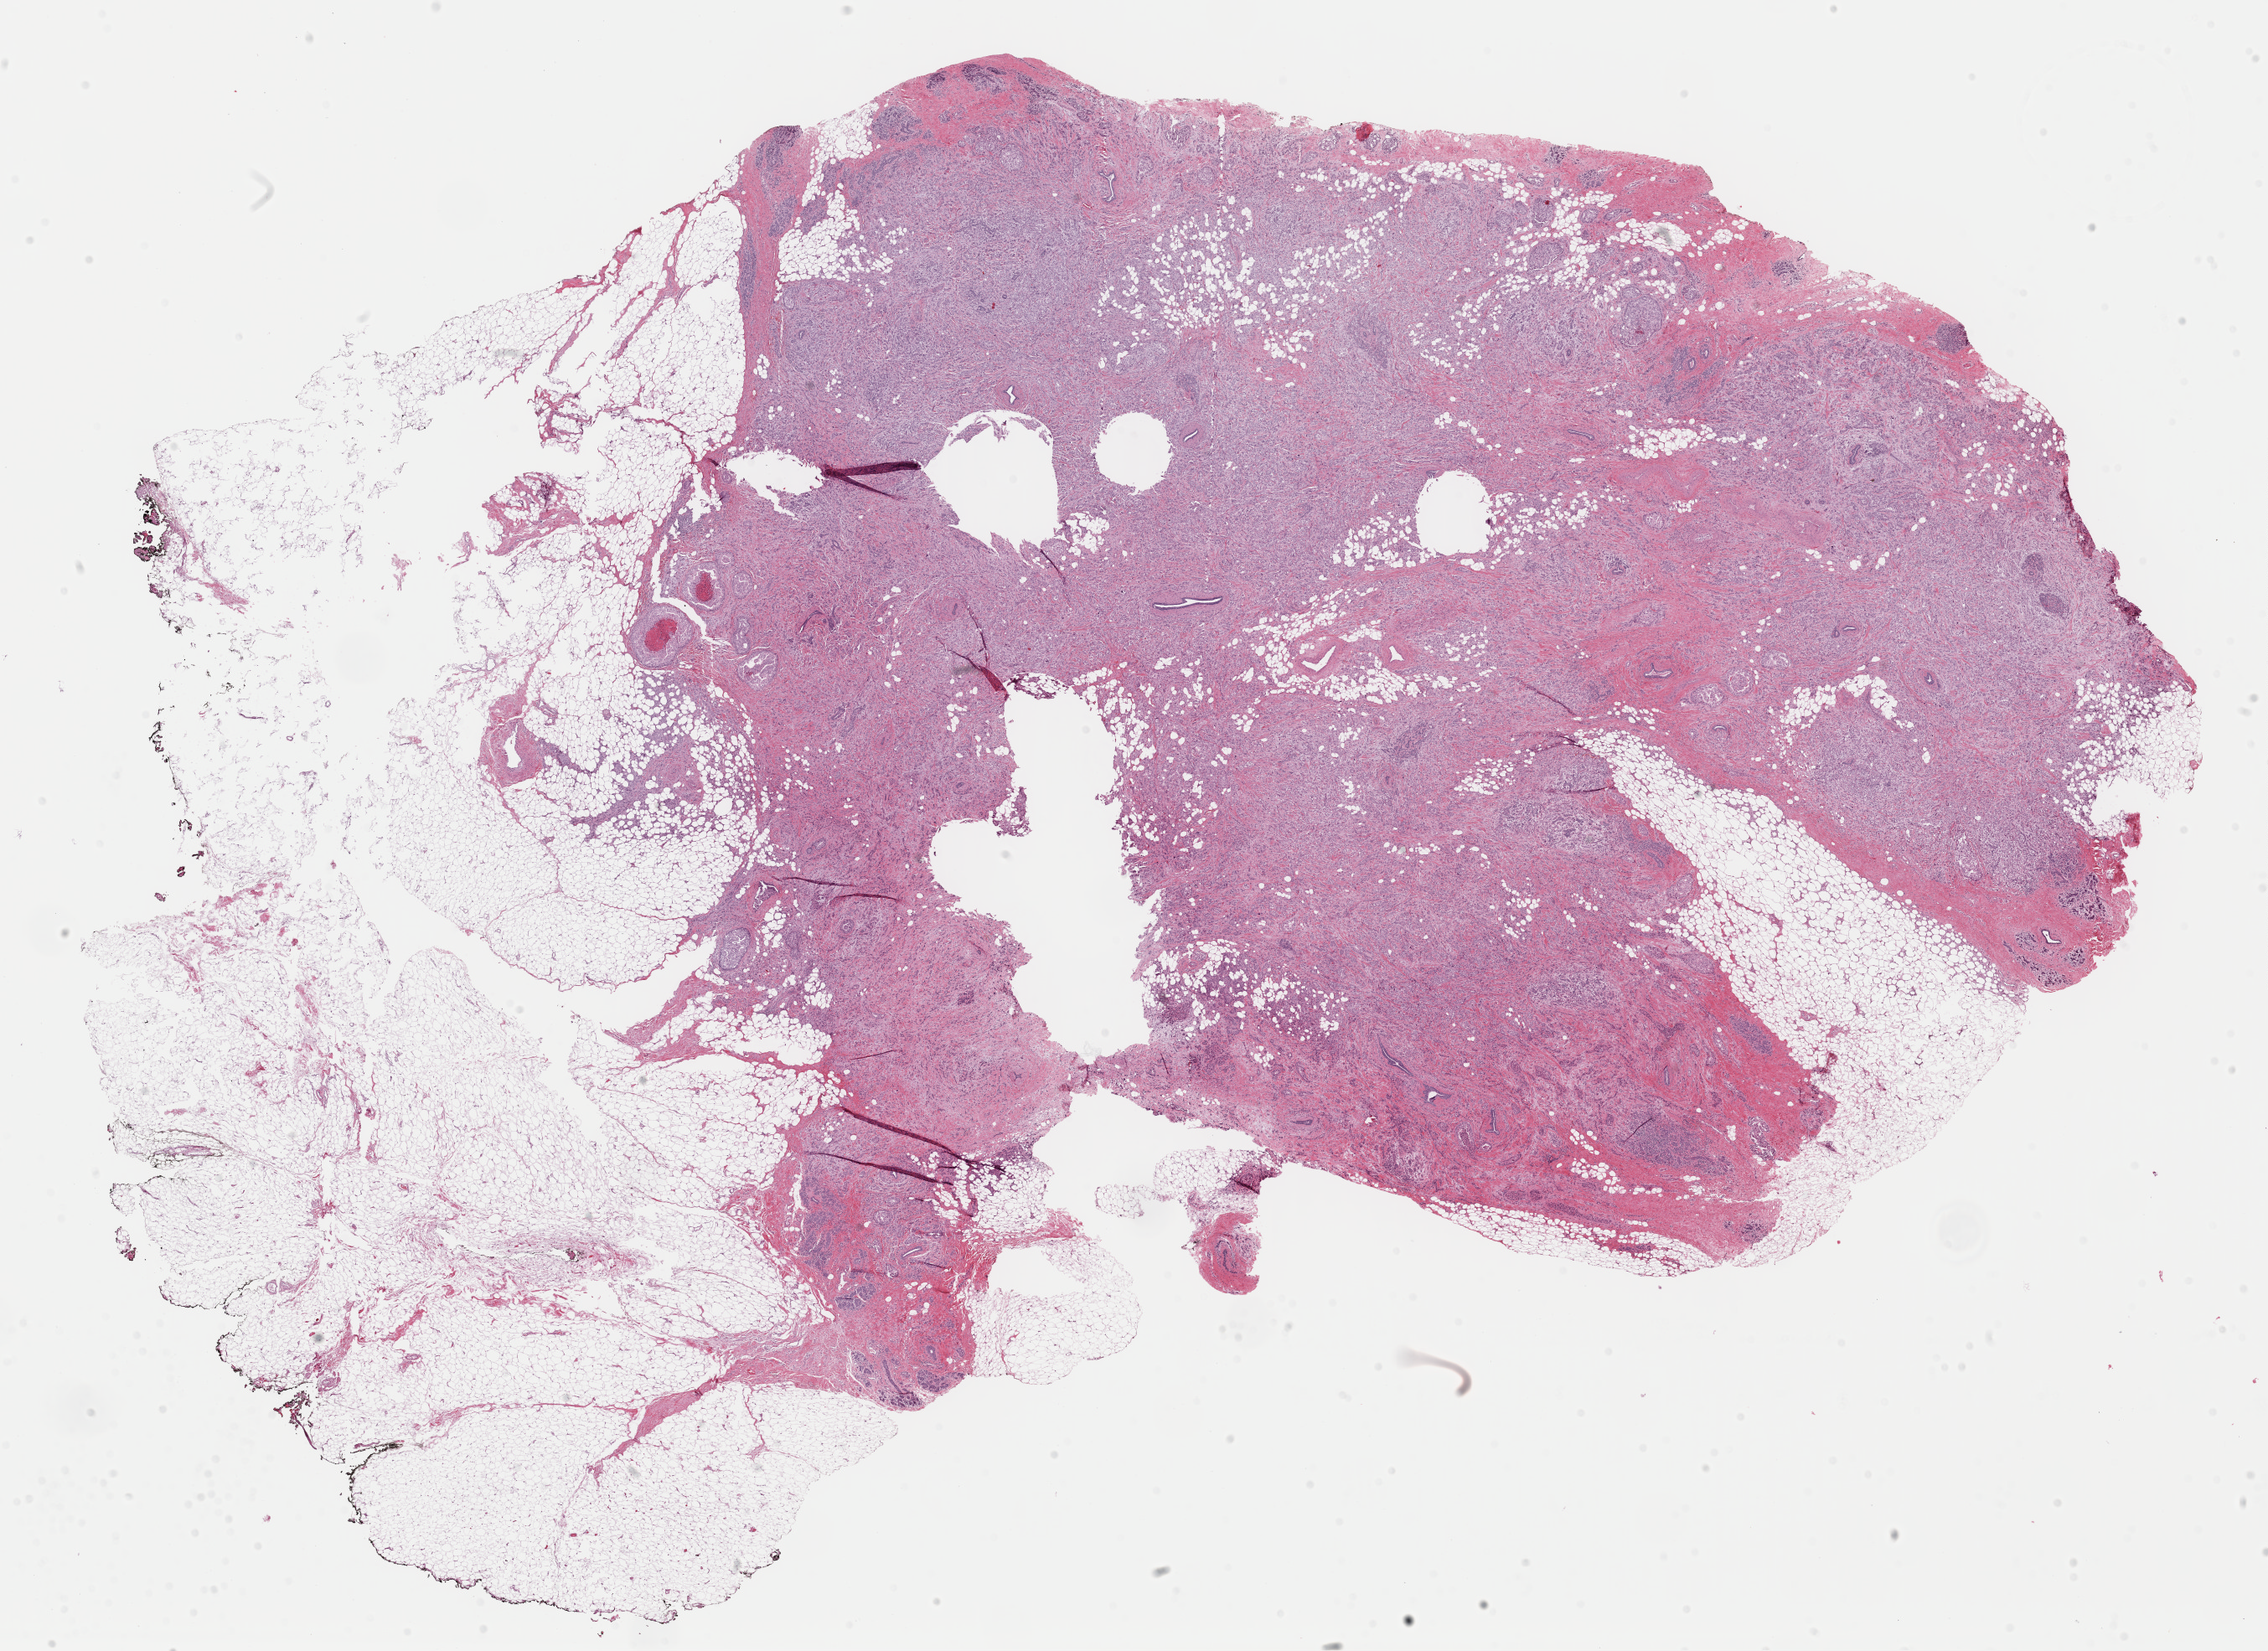
Digitized H&E tissue section (whole slide), shown as a low-resolution overview of the whole scanned area (about 21.4 x 15.6 mm); formalin-fixed paraffin-embedded (FFPE) diagnostic section; primary tumour sample from the breast. Female, age 26 years at initial diagnosis.
AJCC pathologic stage: IIB (6th edition). Pathologic diagnosis: Infiltrating duct carcinoma, NOS. Lymph nodes positive (case pathology): 2 of 12 examined.